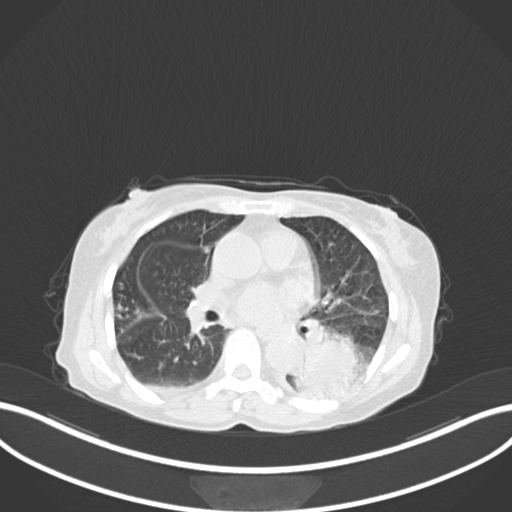
Chest CT, one axial slice. Slice 82 of 233 in the series (ordered by position). Reconstruction kernel B30f. 120 kVp. Lung window (W 1500 / L -600 HU). 1 mm slice thickness. 512 × 512 image matrix, field of view 400 × 400 mm. Patient: female, 78 years. From the clinical record (not read from this slice): clinical TNM (as recorded): T3 N0 M1.
Structures marked on this image (rectangle marked by the reading radiologist):
- lung tumour (recorded histology: squamous cell carcinoma): bounding box <293,329,361,396> (left, top, right, bottom; pixels)